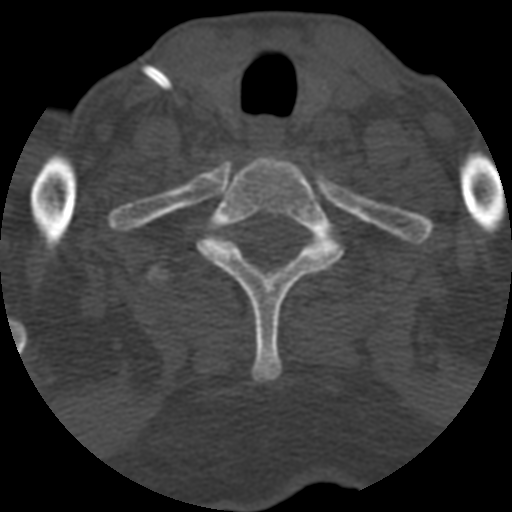
CT including the spine, one axial slice; slice 517 of 708 in the series (ordered by position); reconstruction kernel STANDARD; one of 3 acquisitions stored at this slice position; bone window (W 1800 / L 400 HU); 1.25 mm slice thickness; 512 × 512 image matrix, field of view 160 × 160 mm. Patient age 55 years. From the clinical record (not read from this slice): primary cancer: colon; vertebrae with lytic lesions (as recorded): T12, L1, L5.
Structures marked on this image (semi-automatically segmented with operator editing):
- T1 vertebra: bounding box (x1, y1, x2, y2) in pixels: (197, 154, 344, 382)
- T2 vertebra: (150, 236, 238, 285)